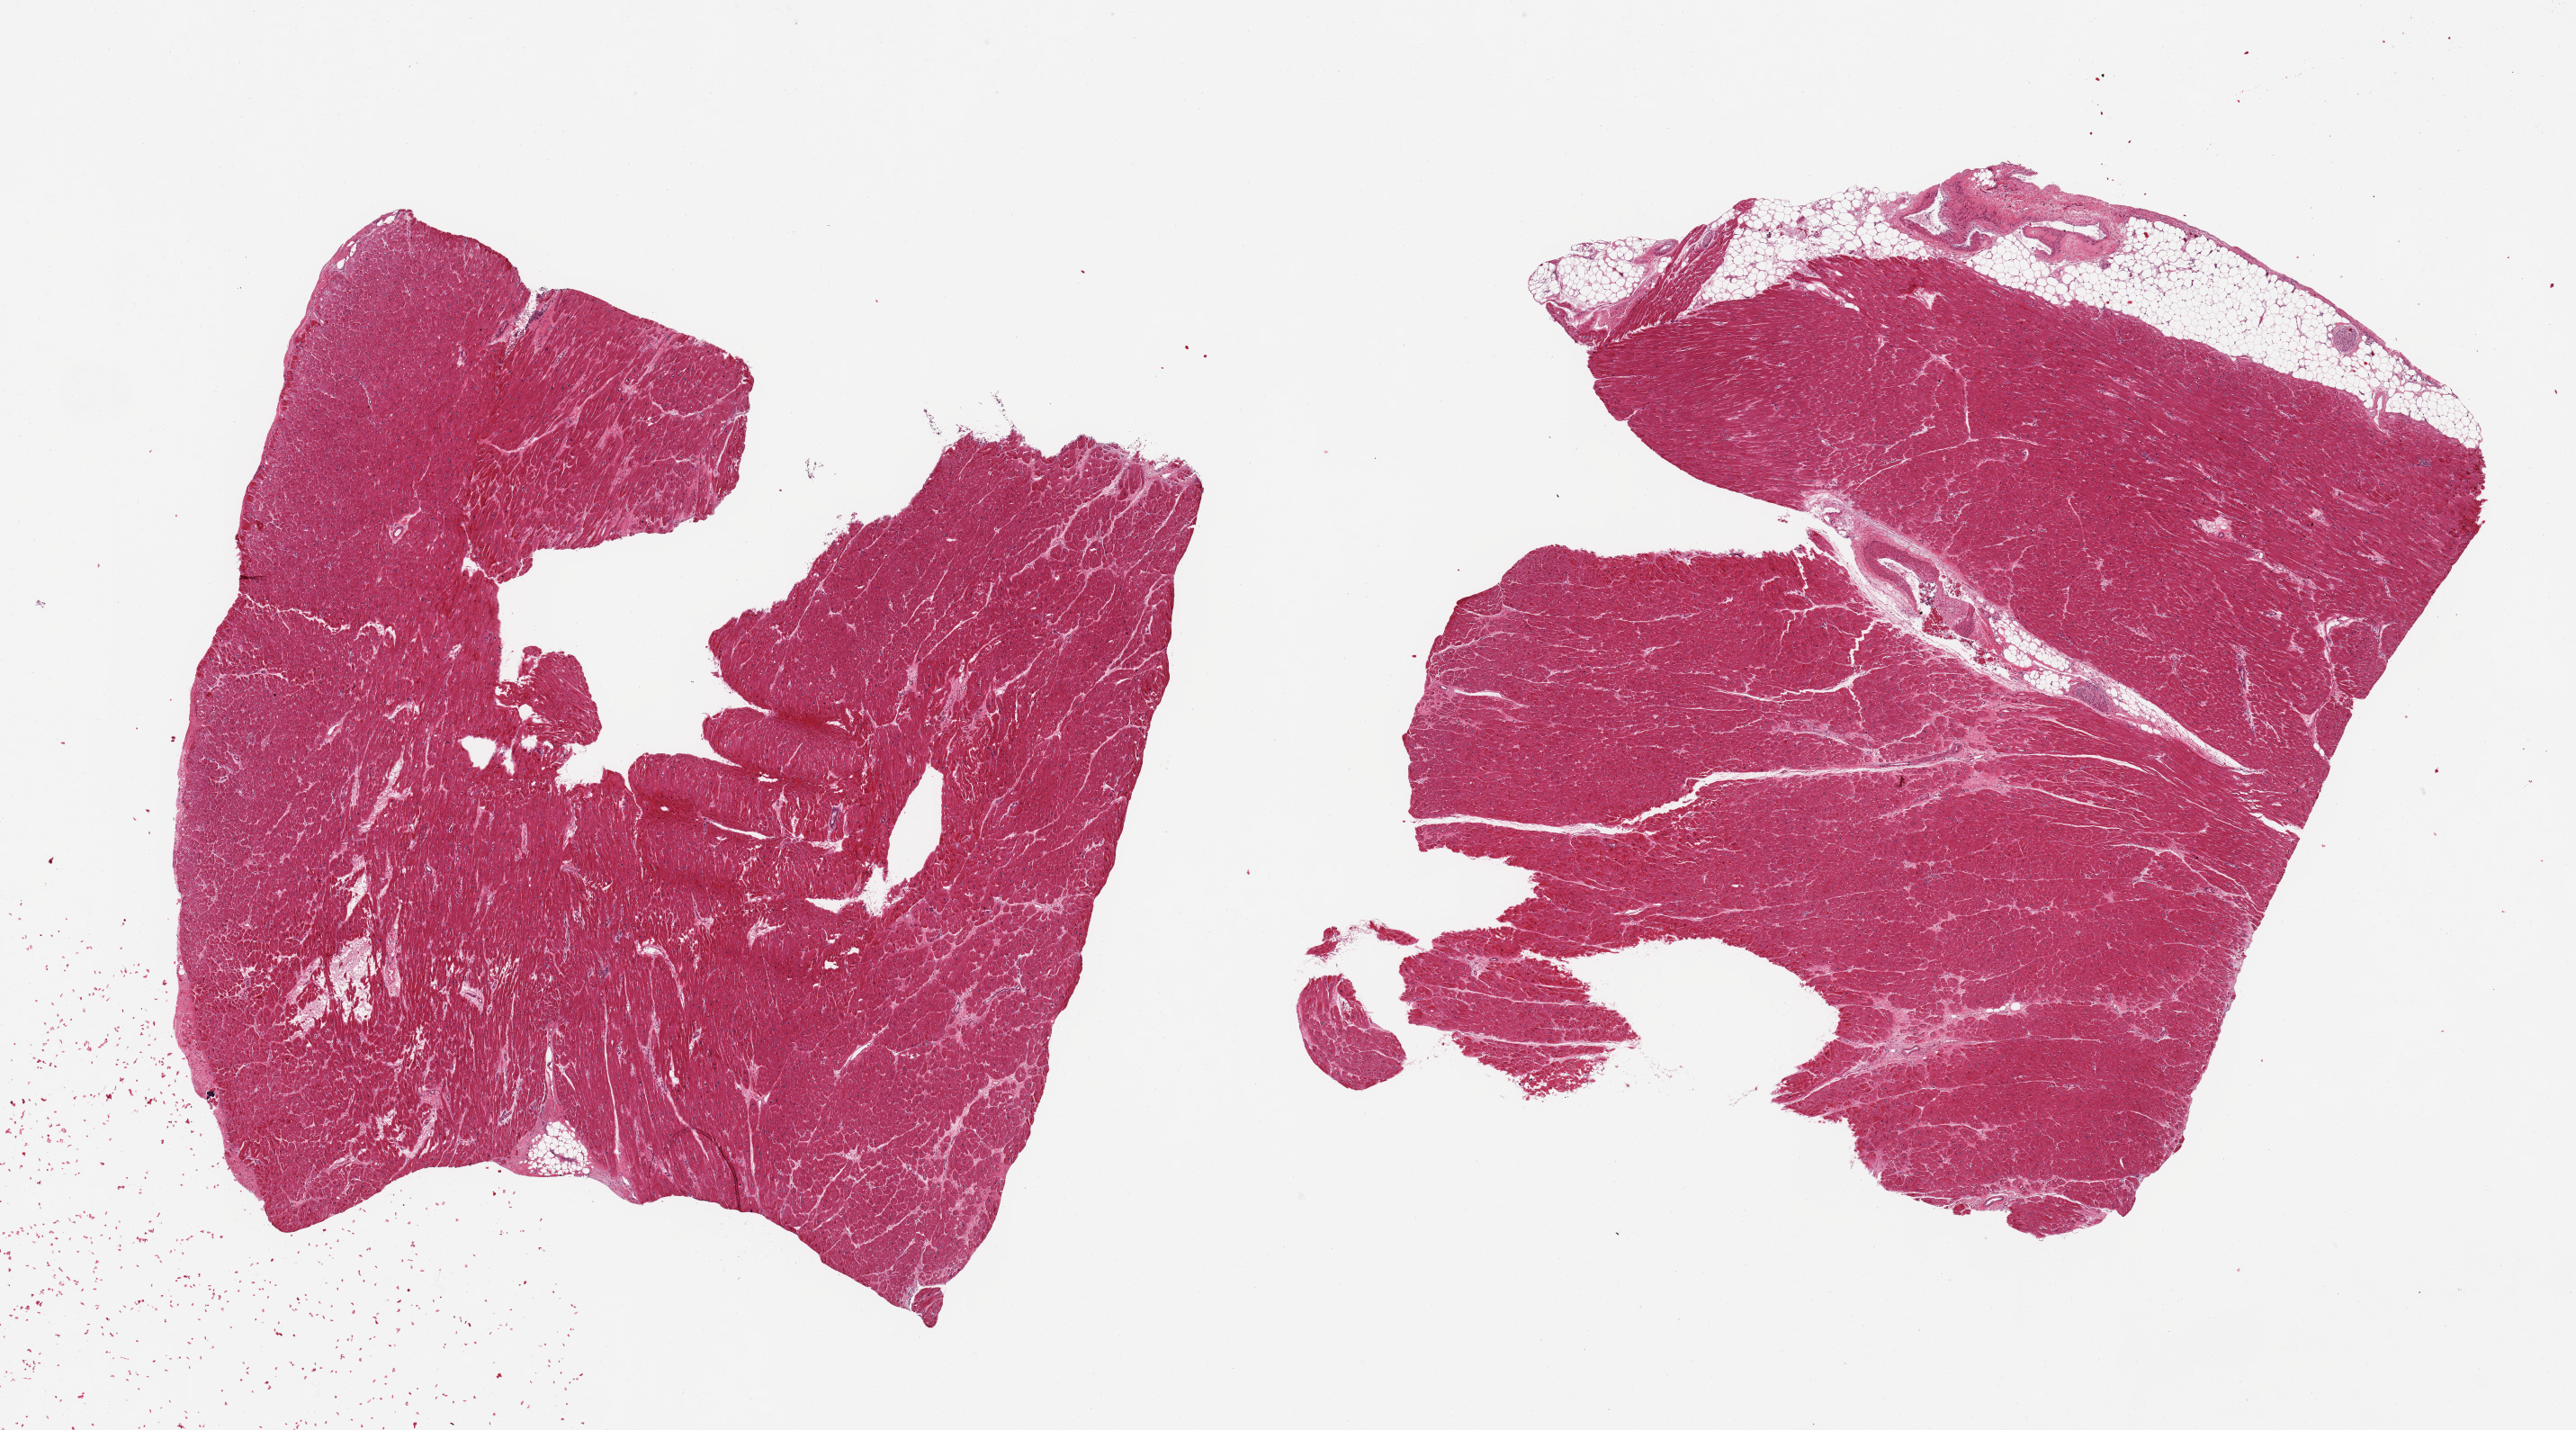
H&E whole-slide image, a low-resolution overview of the entire scanned area, about 22.6 x 12.6 mm (slide scanned at 20x), PAXgene-fixed paraffin-embedded (PFPE) section, target tissue: heart, tissue donor sample.
Reviewer comment on this tissue sample: 2 pieces; mild interstitial fibrosis with focal scarring, some hypertrophy.